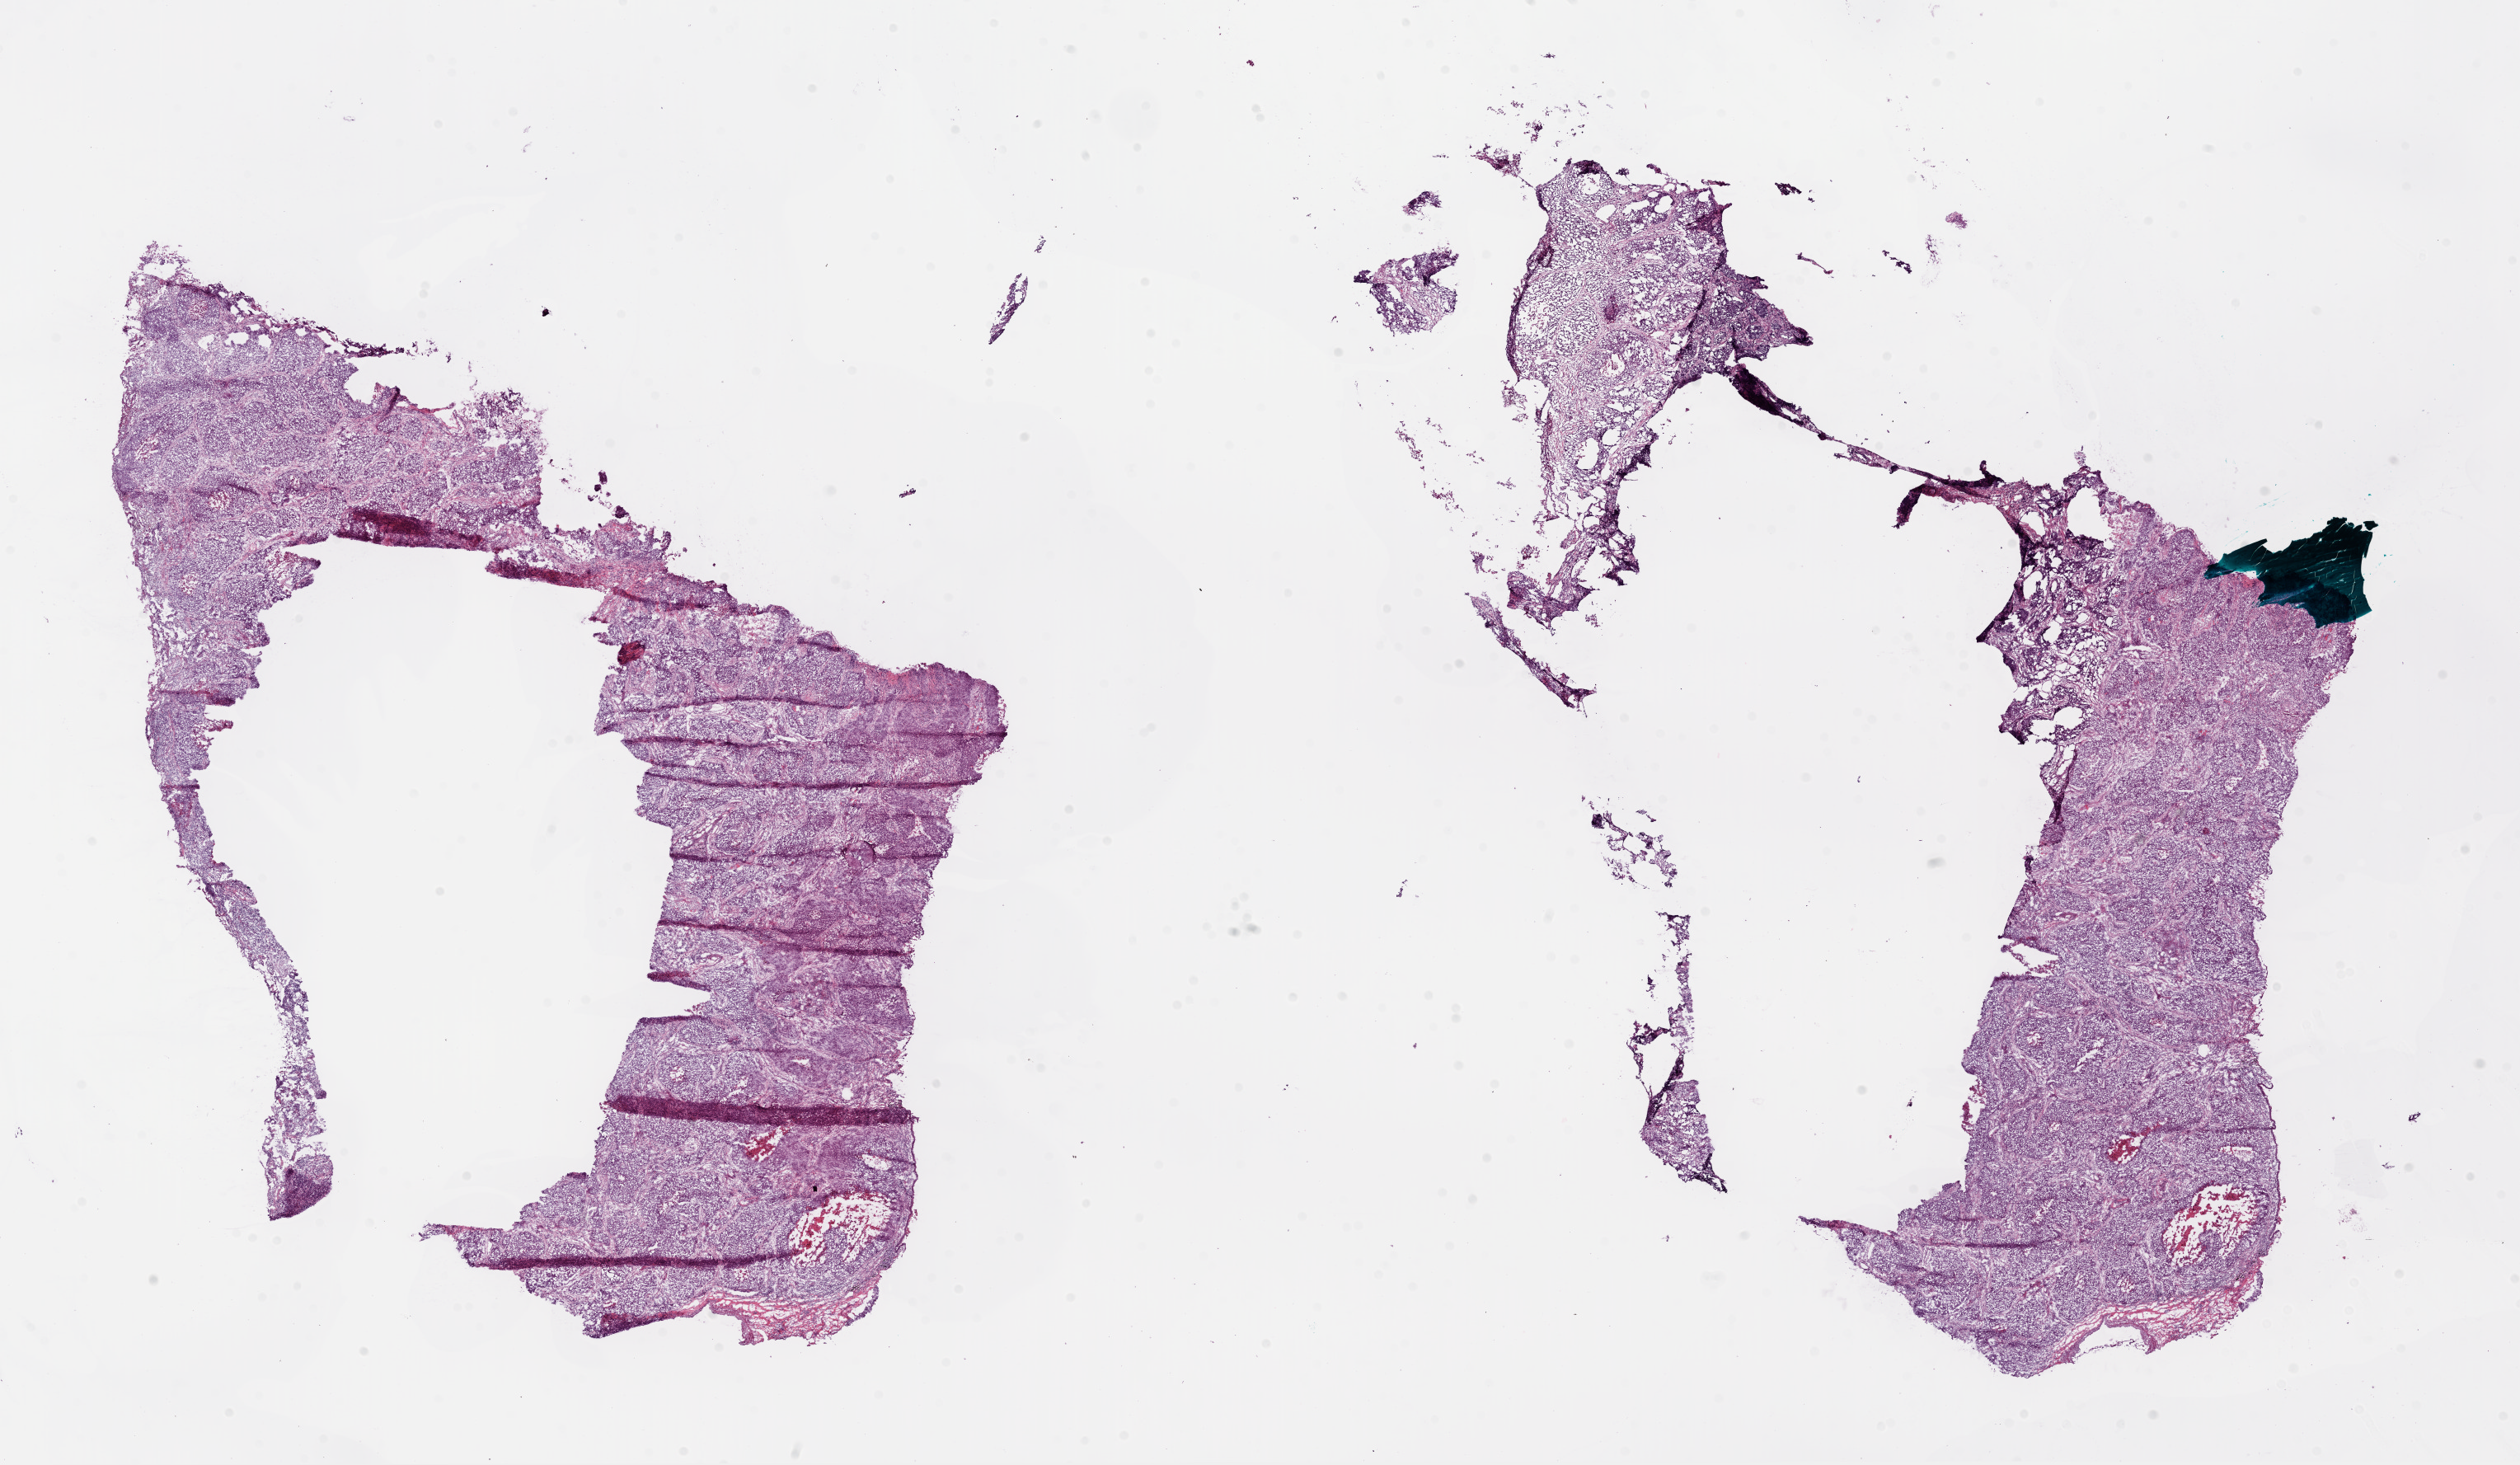
Whole-slide histology image, H&E — low-resolution overview of the scanned area, about 24.7 x 14.3 mm (from a 20x scan). Frozen section. Sample: primary tumour, lung. Male patient; age at initial diagnosis 75 years. Pathologist review of this section (percent, as recorded): tumour nuclei 95%, necrosis 0%.
AJCC pathologic stage: IA. Laterality: left. Diagnosis: Squamous cell carcinoma, NOS (upper lobe, lung).